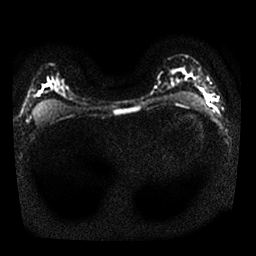
Breast MRI, one axial slice; slice 16 of 25 in the series (ordered by position); diffusion-weighted series; image 2 of 4 stored at this slice position (different b-values; order by instance number); 1.5 T; 256 × 256 image matrix, field of view 320 × 320 mm. Female patient.
Annotated regions visible in this slice (outlined manually by an expert reader):
- tumour on diffusion-weighted imaging: bounding box [x1, y1, x2, y2] px = [207, 95, 211, 99]